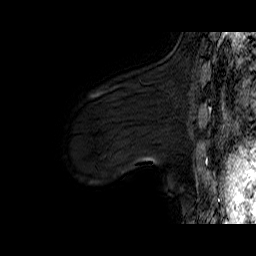
Breast MRI (dynamic contrast-enhanced), one sagittal slice. Position 12 of 60 along the scan axis. Dynamic contrast-enhanced series, time point 2 of 6 at this slice position (early post-contrast). 1.5 T. TE 6.4 ms, TR 32.9 ms. 4 mm slice thickness. 256 × 256 image matrix, field of view 200 × 200 mm. Female patient. From the clinical record (not read from this slice): setting: breast cancer imaged before/during neoadjuvant chemotherapy; receptor status: HER2-positive.
Structures marked on this image (semi-automatically segmented with operator editing):
- analysis volume of interest (the breast-tissue region the enhancement analysis was run in; not a lesion): bounding box (x1, y1, x2, y2) in pixels: (78, 94, 152, 149)
- tumour enhancement mask (voxels above the 100 % enhancement threshold inside the analysis volume of interest): (89, 94, 99, 98)